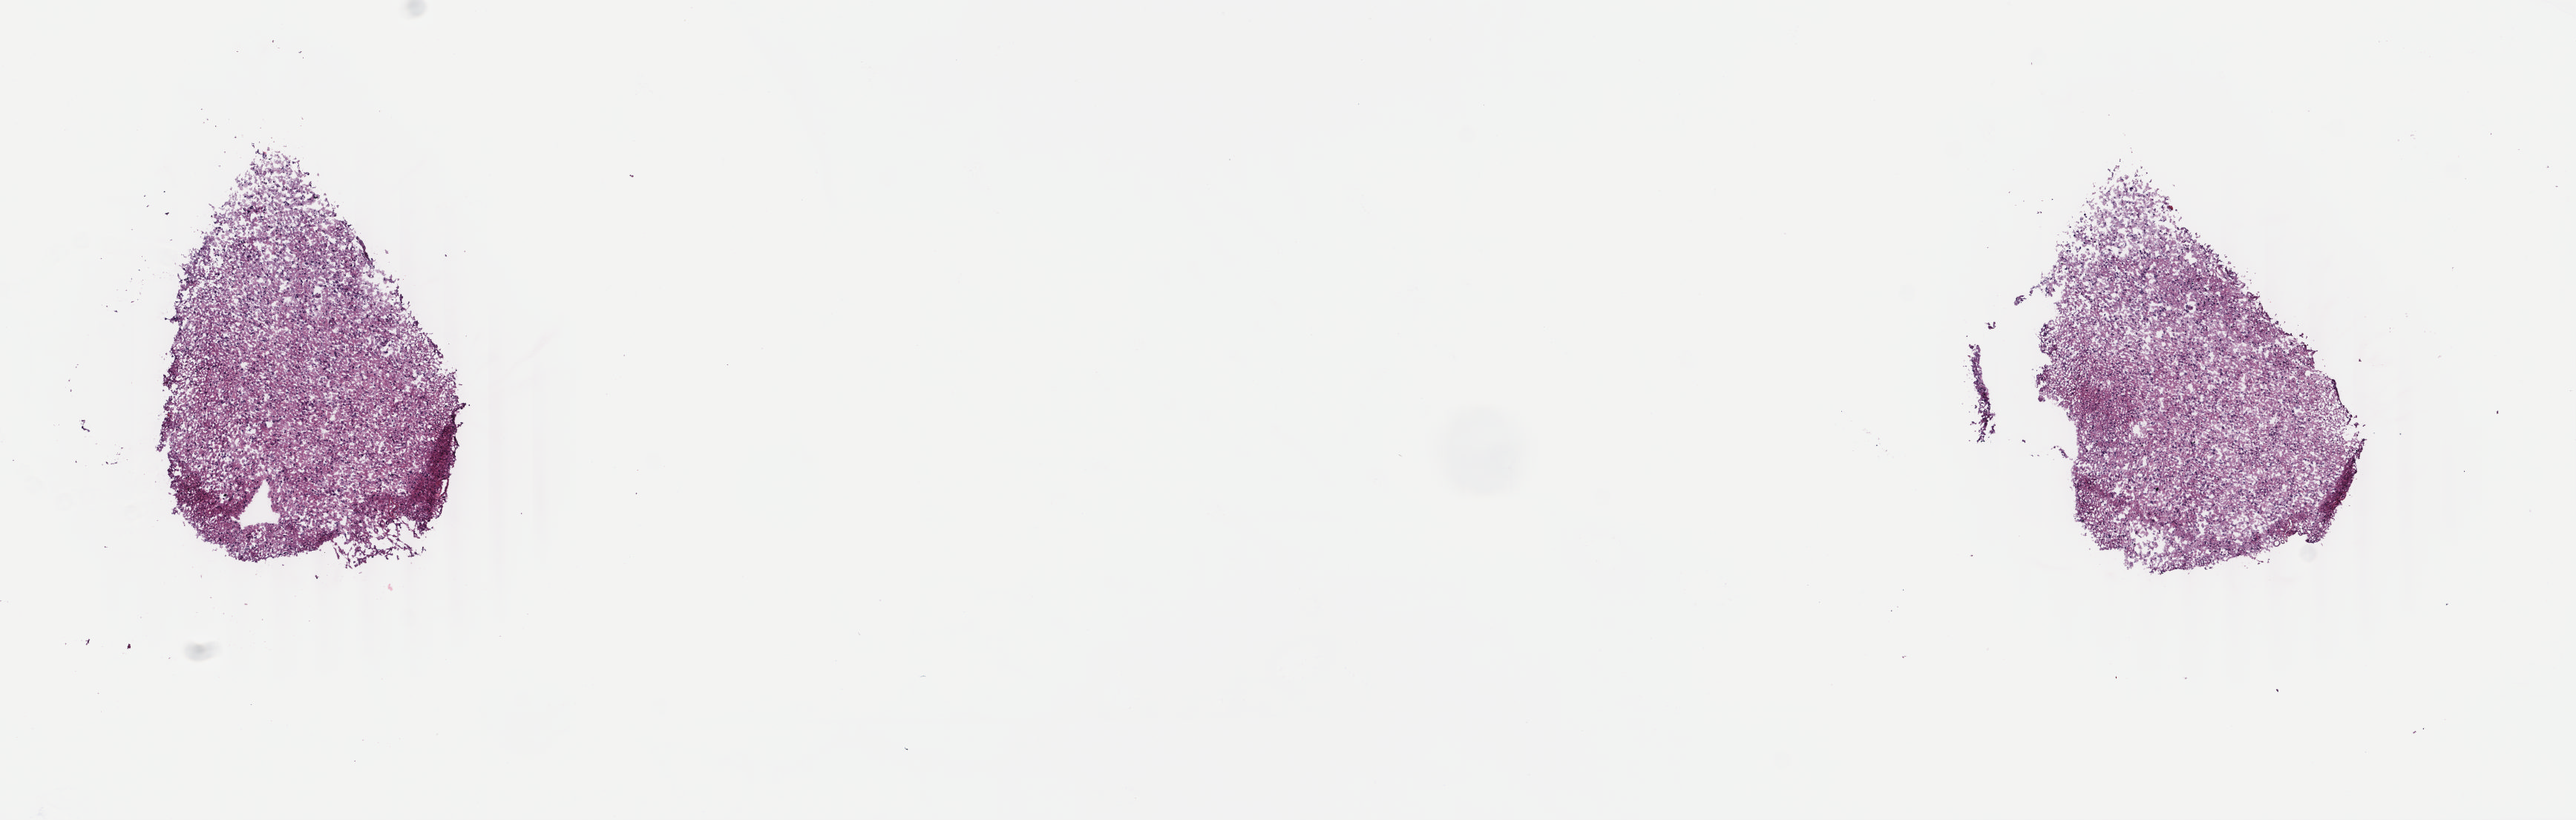
Whole-slide histology image, H&E-stained — shown as a low-resolution overview of the whole scanned area (about 13.8 x 4.4 mm, slide scanned at 40x). Frozen section from the top of the tissue portion. Sample: primary tumour, brain. Patient: female, age at initial diagnosis 44 years. Composition of this section per pathologist review: tumour cells 80%, tumour nuclei 80%.
Diagnosis: Mixed glioma (parietal lobe).